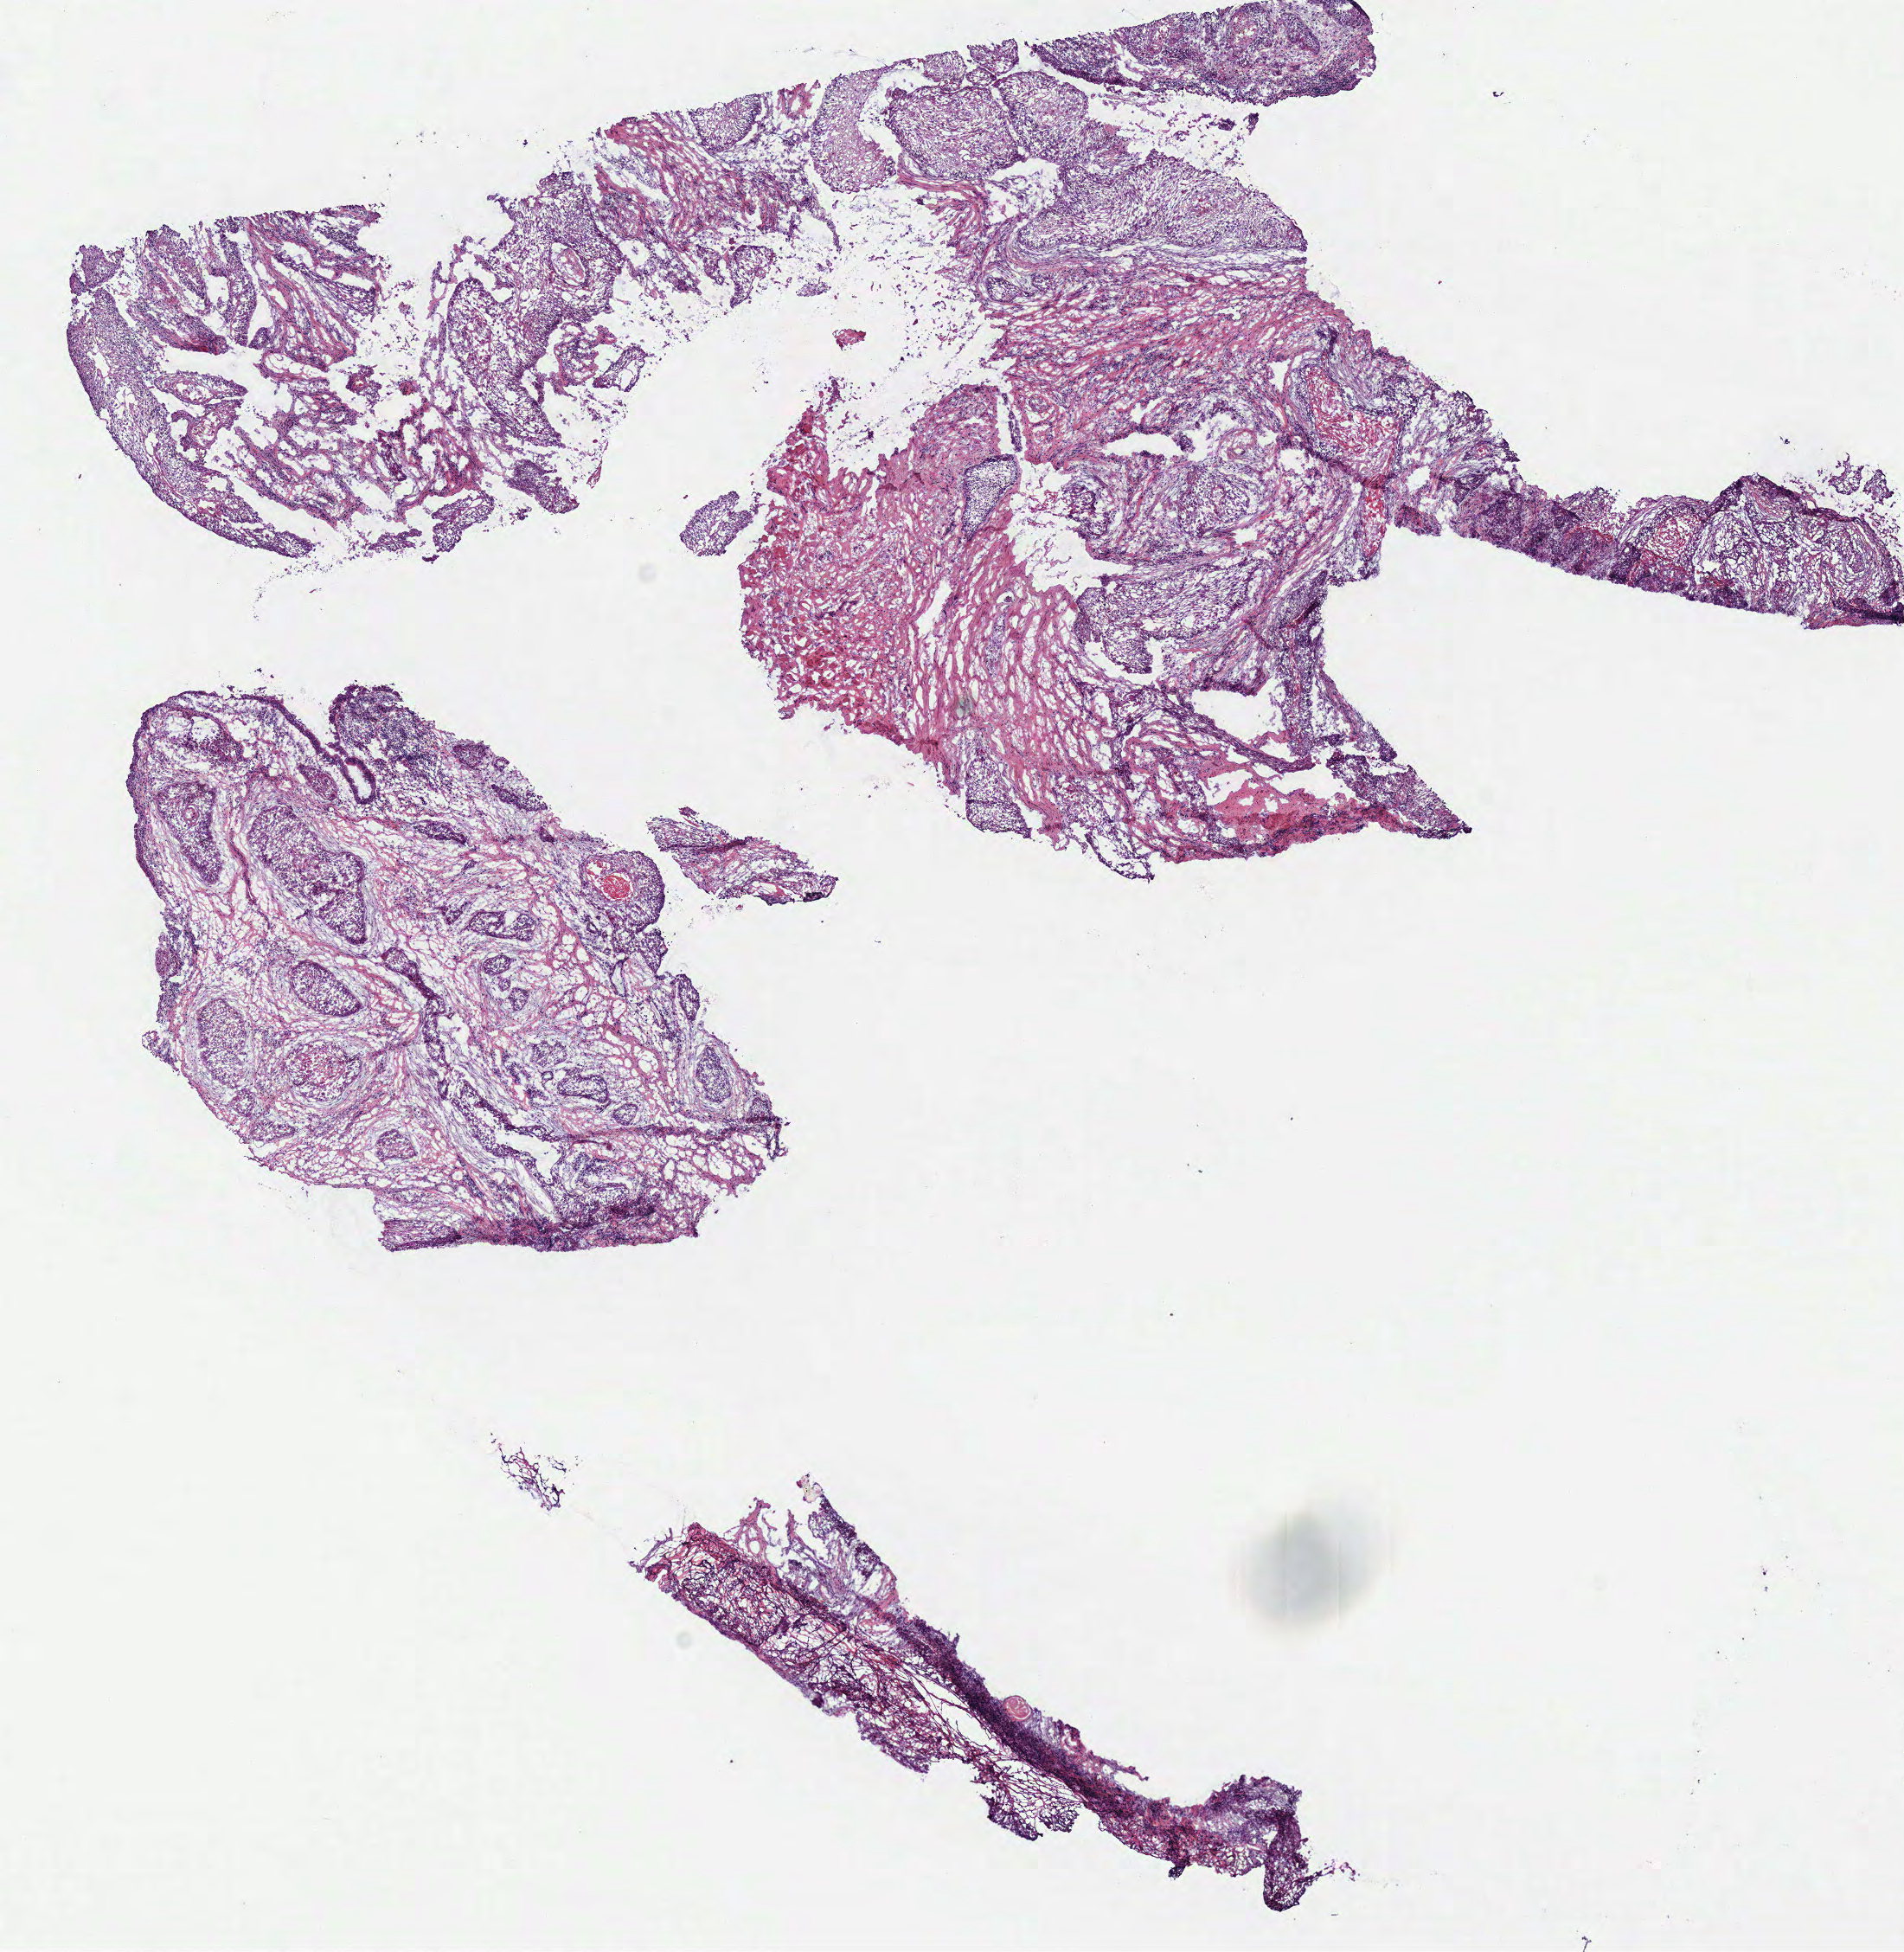
H&E-stained whole-slide image — shown as a low-resolution overview of the whole scanned area (about 8.7 x 8.9 mm), frozen section, head and neck, primary tumour sample. Female patient; age at initial diagnosis 82 years. Histologic grade: G2 (moderately differentiated). Pathologist review of this section (percent, as recorded): tumour cells 55%, tumour nuclei 70%, normal cells 0%, stromal cells 45%, necrosis 0%. Inflammatory infiltration, as recorded: lymphocyte infiltration 10%, monocyte infiltration 0%, neutrophil infiltration 0%.
AJCC pathologic stage: II. TNM: T2 NX. Pathologic diagnosis: Squamous cell carcinoma, NOS (larynx, NOS).